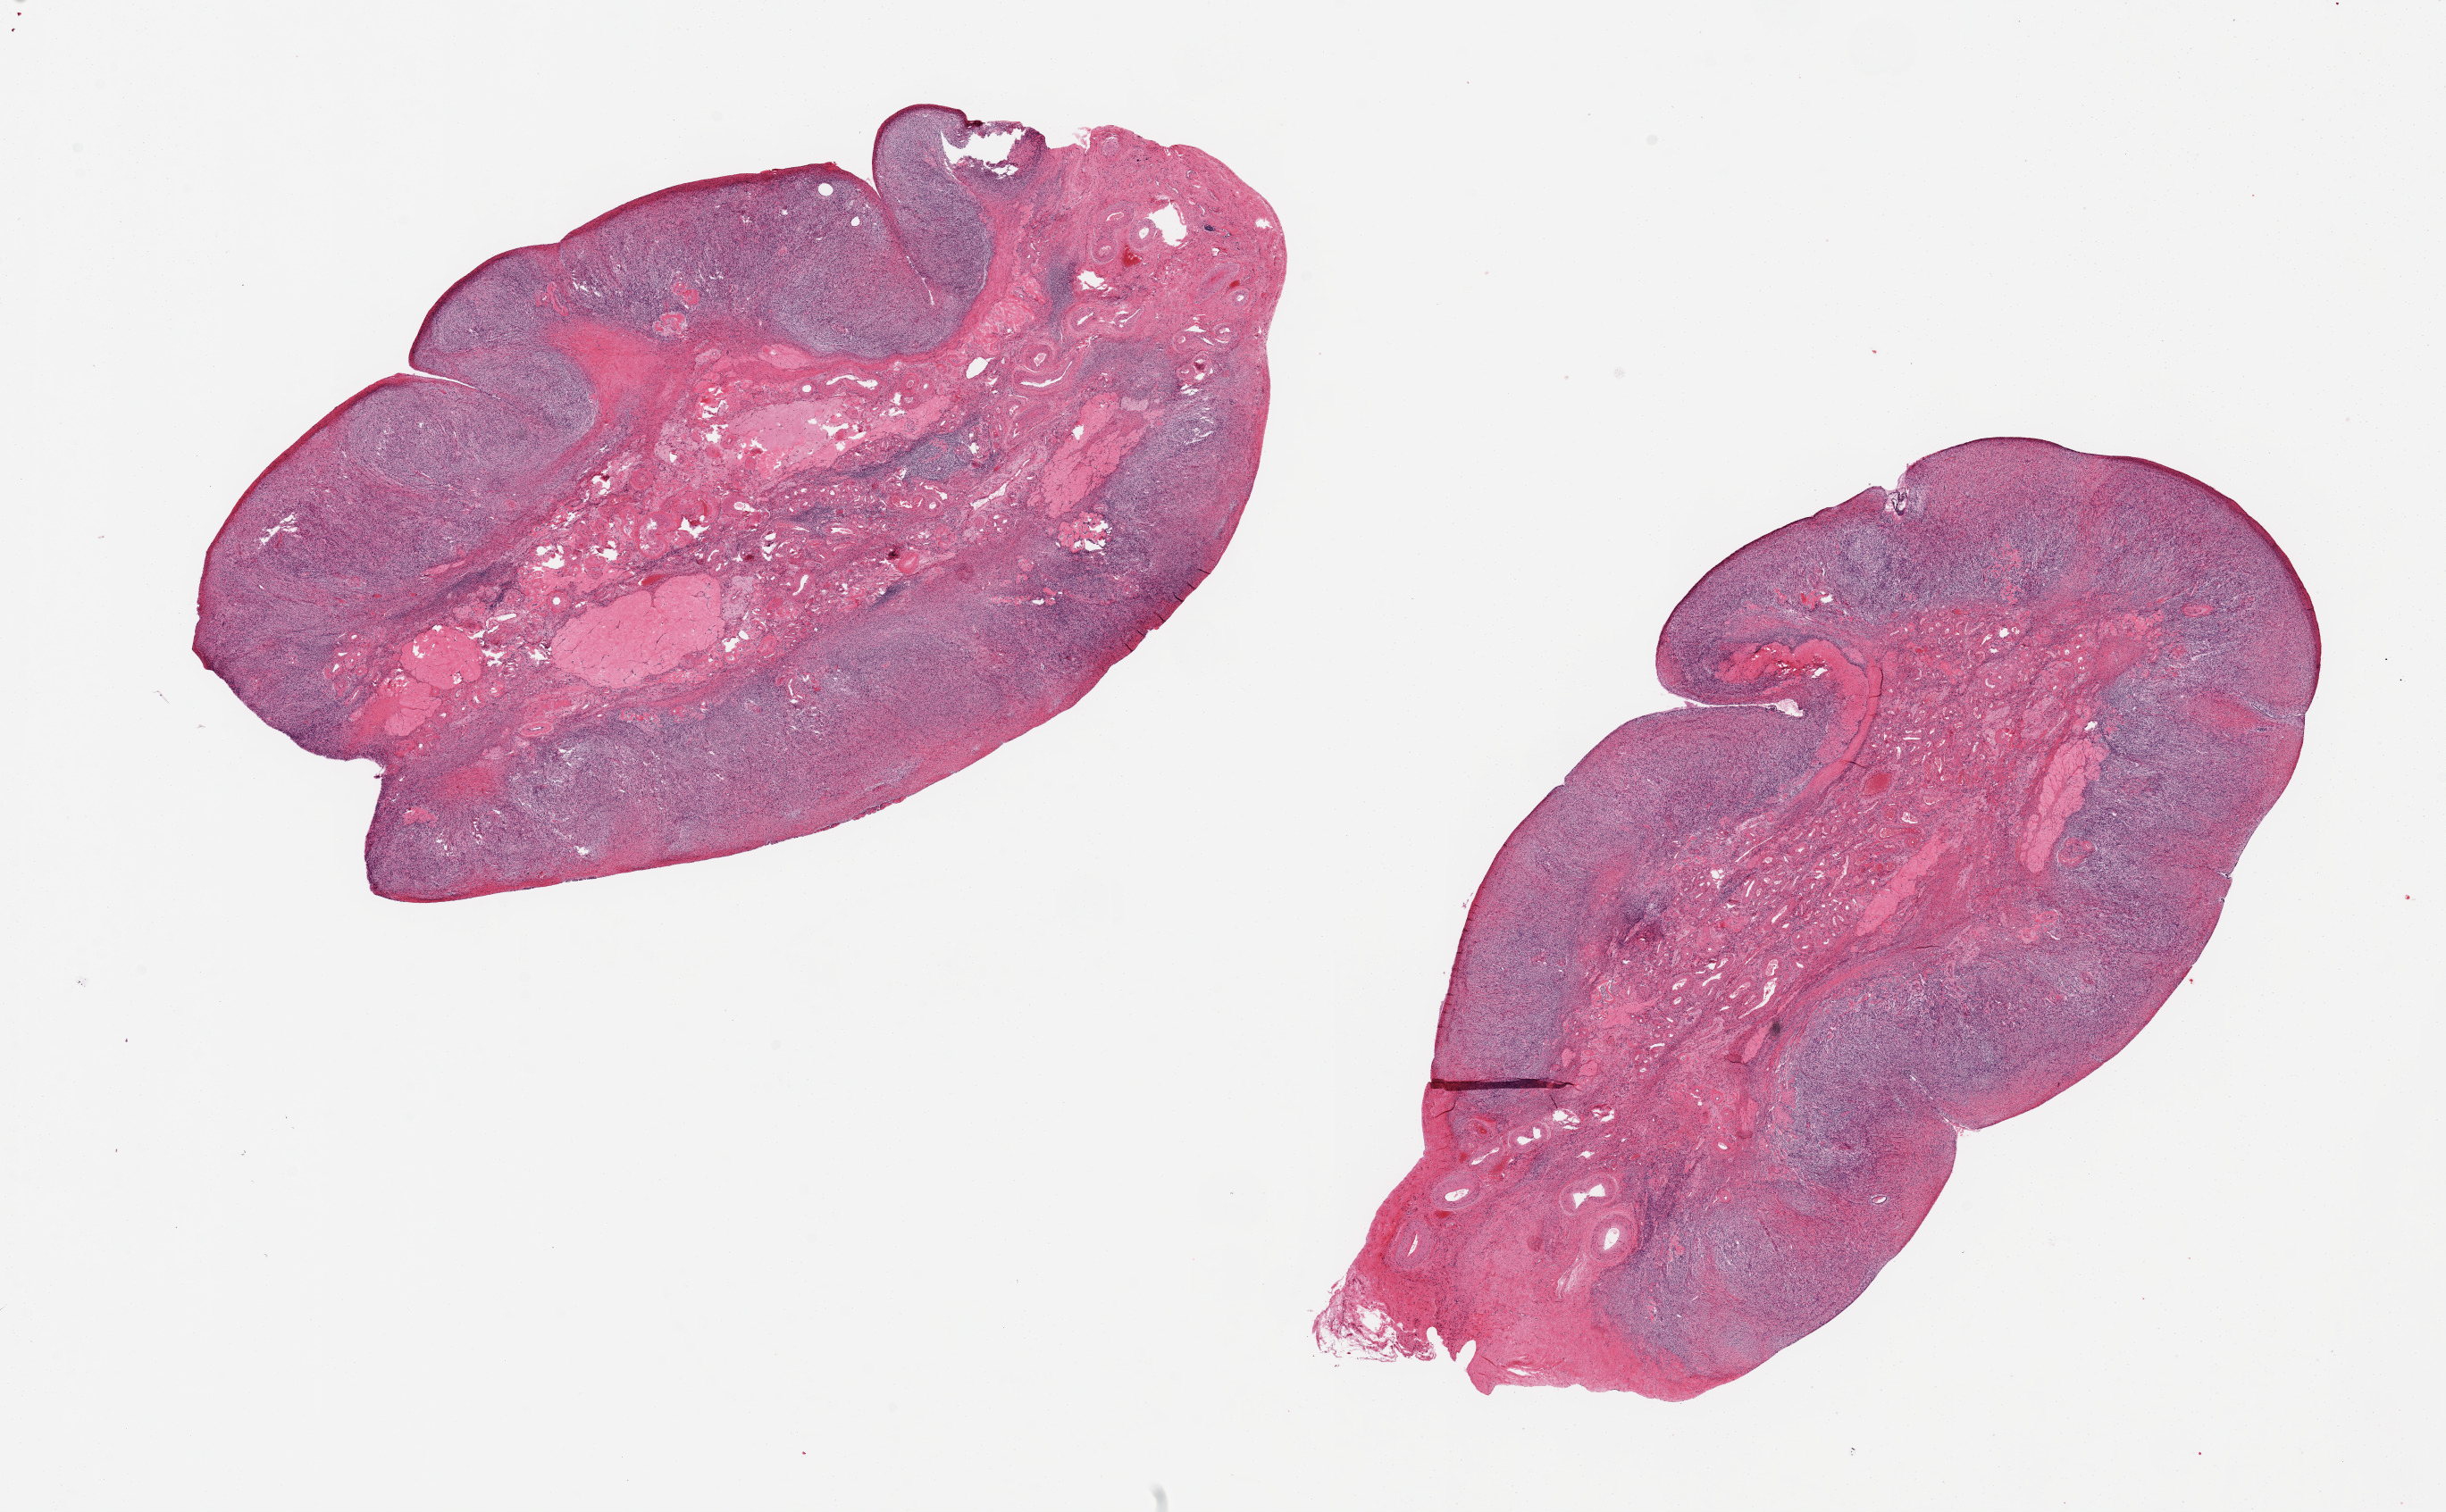
Whole-slide image, haematoxylin and eosin stain, brightfield — a low-resolution overview of the entire scanned area, about 21.7 x 13.4 mm (slide scanned at 20x); PAXgene-fixed paraffin-embedded (PFPE) section; target tissue: ovary; donor tissue sample. Donor sex: female.
• pathologist's review note for this sample: 2 pieces, 10x6 & 10x5 mm; corpora albicans; no ova